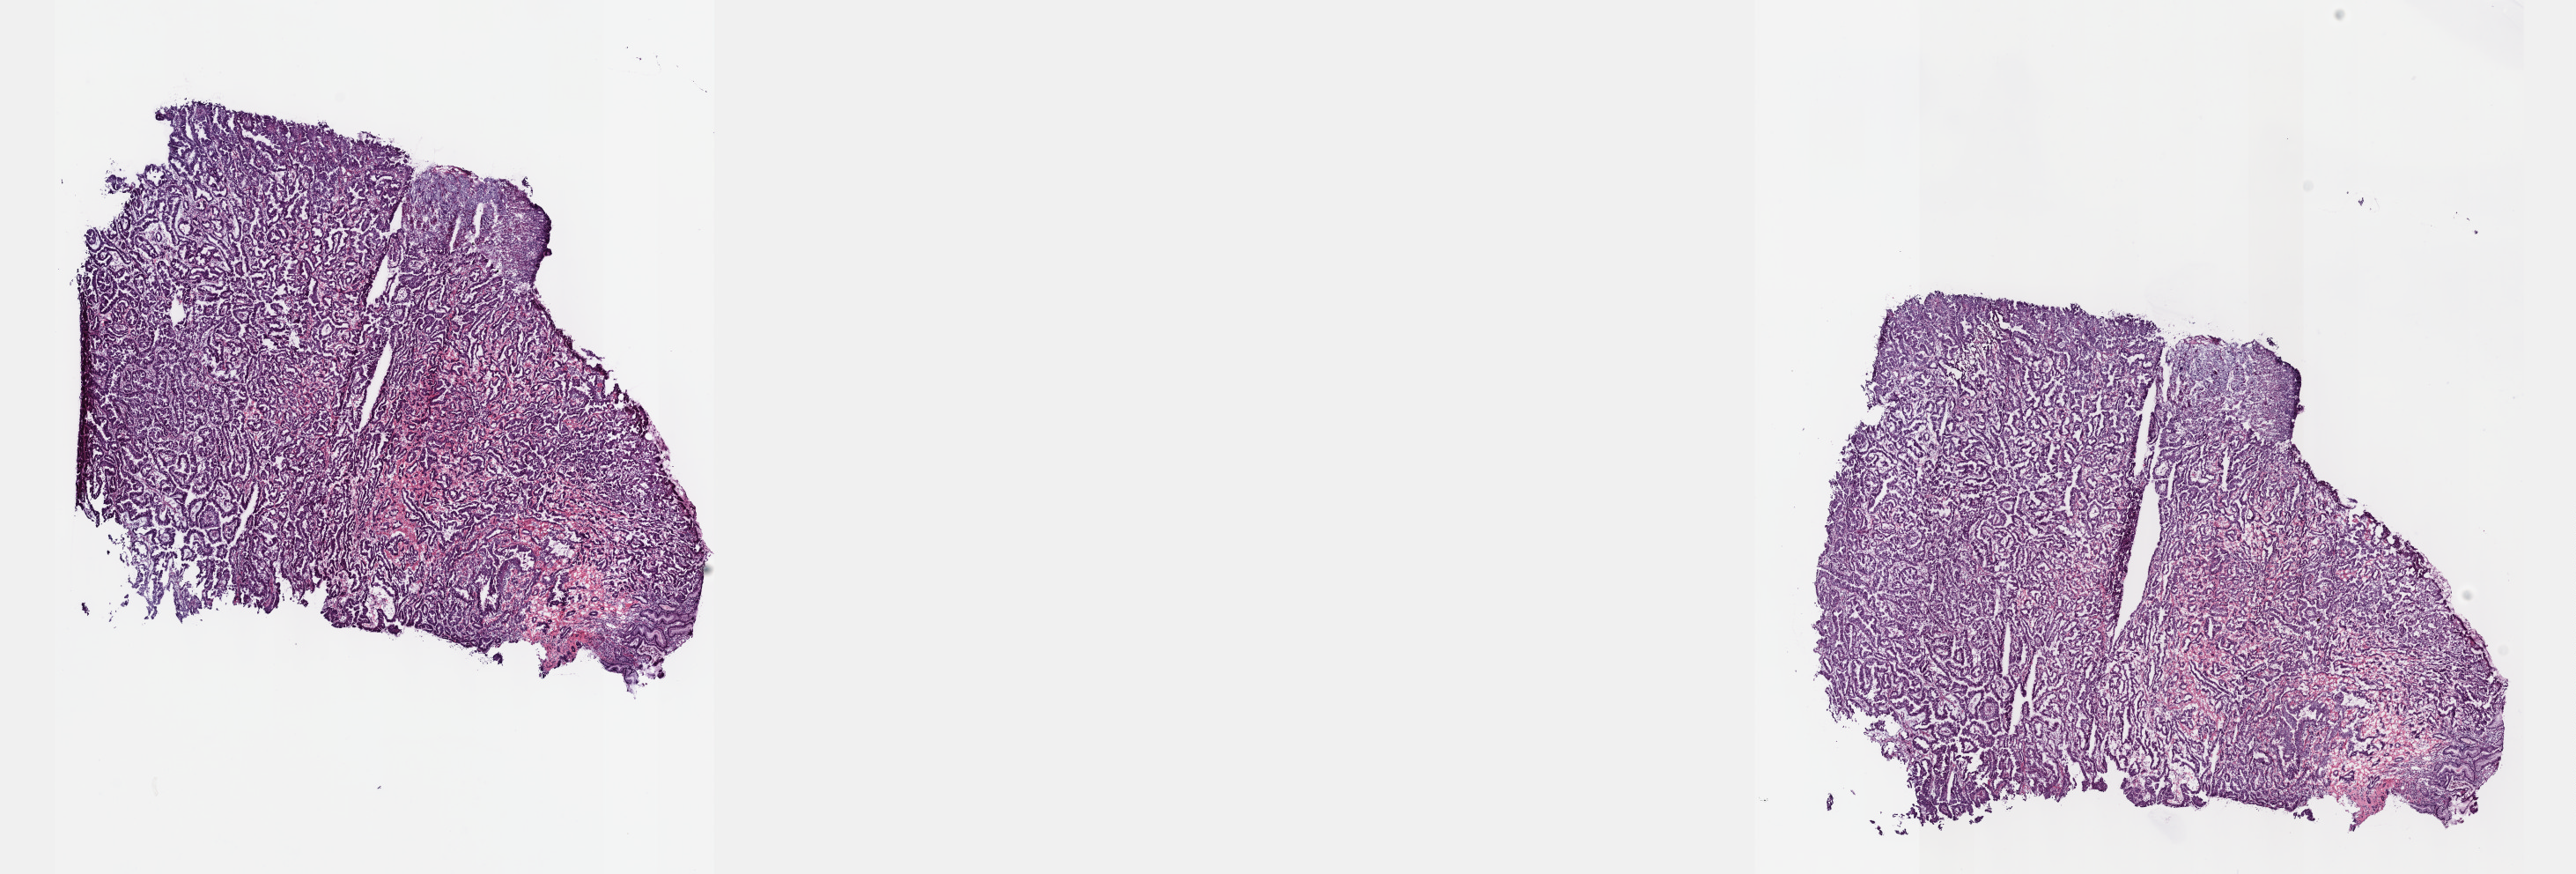
Whole-slide histology image, H&E, low-resolution overview of the scanned area, about 23.6 x 8.0 mm (acquisition: 40x scan), frozen section from the top of the tissue portion, stomach, primary tumour sample. Patient: male, age at initial diagnosis 56 years. Histologic grade: G2 (moderately differentiated). Pathologist review of this section (percent, as recorded): tumour cells 70%, tumour nuclei 70%, normal cells 0%, stromal cells 30%, necrosis 0%. Infiltration values recorded for this section: lymphocyte infiltration 40%, monocyte infiltration 20%, neutrophil infiltration 20%.
- histologic diagnosis: Adenocarcinoma, intestinal type (cardia, NOS)
- AJCC pathologic stage: IIIC (7th edition)
- lymph nodes positive (case pathology): 8 of 26 examined